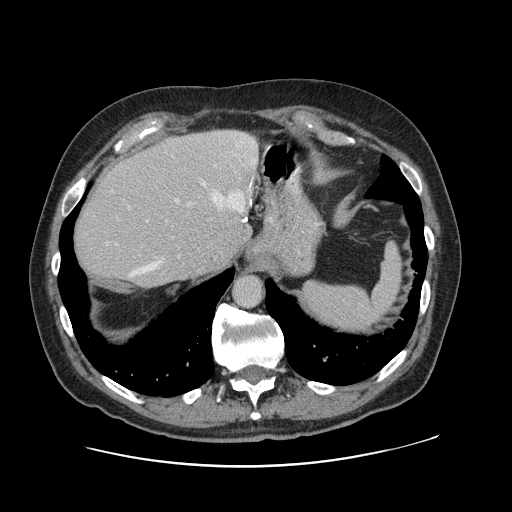
Contrast-enhanced abdominal CT, one axial slice. Intravenous contrast given. Soft-tissue window (W 400 / L 40 HU). 512 × 512 image matrix, field of view 402 × 402 mm. Male patient, age 71 years. From the clinical record (not read from this slice): diagnosis: colorectal cancer liver metastases, imaged before liver resection; multiple liver metastases: no; largest metastasis: 3.3 cm; disease in both lobes: no.
Outlined on this slice (outlined manually by an expert reader):
- hepatic veins: bounding box <131,182,250,276> (left, top, right, bottom; pixels)
- liver: <74,131,258,288>
- planned liver remnant (the part of the liver to remain after resection): <74,156,239,288>